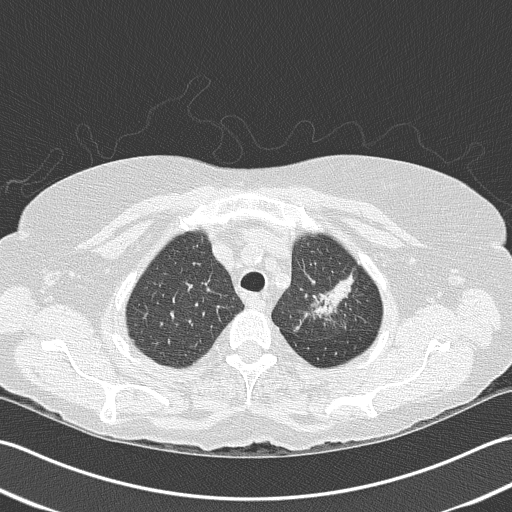
Low-dose screening chest CT, axial slice. Baseline annual screen. Lung window (W 1500 / L -600 HU). 2 mm slice thickness. Slice 131 of 159 in the series. 512 × 512 image matrix. Female, age 68 years at enrolment.
Expert reader's lesion annotation, bounding box <292,254,366,328> (left, top, right, bottom; pixels). No non-calcified nodule or mass ≥4 mm was recorded by the screening reader at this exam. Participant outcome: lung cancer diagnosed 763 days after this screen — adenocarcinoma, NOS, left upper lobe, poorly differentiated (G3), stage IB (AJCC 6th edition), 50 mm at pathology.